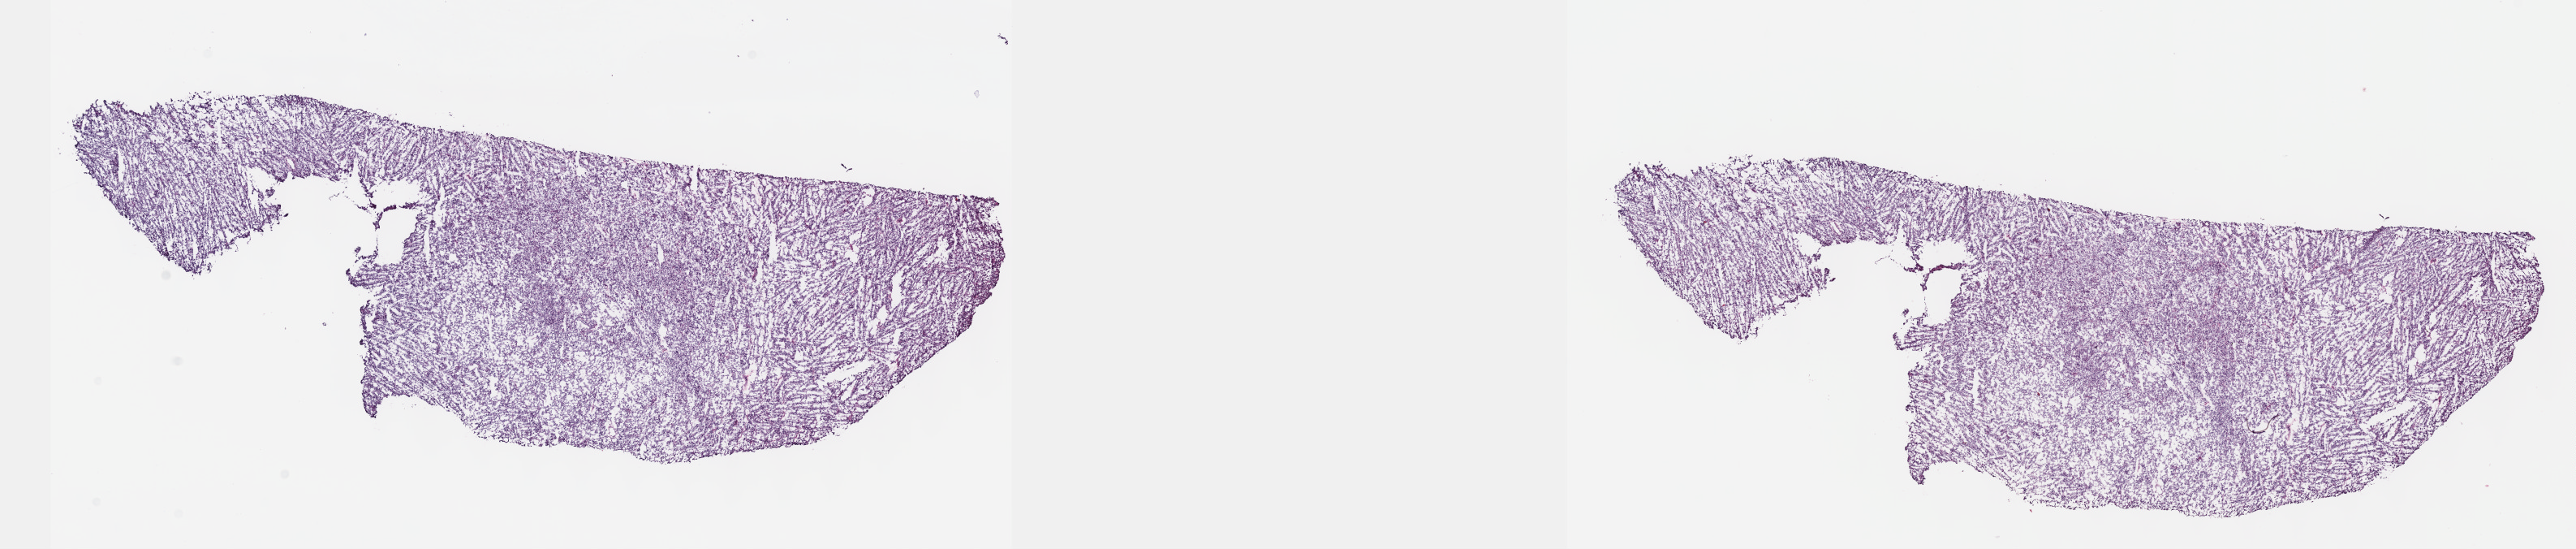
Whole-slide histology image, H&E-stained — a low-resolution overview of the entire scanned area, about 25.7 x 5.5 mm (slide scanned at 40x); frozen section; sample: primary tumour, uterus. Female patient; age at initial diagnosis 58 years. Slide review estimates, as recorded: tumour cells 100%, tumour nuclei 80%, normal cells 0%, stromal cells 0%, necrosis 0%. Inflammatory infiltration, as recorded: lymphocyte infiltration 1%, monocyte infiltration 0%, neutrophil infiltration 0%.
Histologic diagnosis: Leiomyosarcoma, NOS.